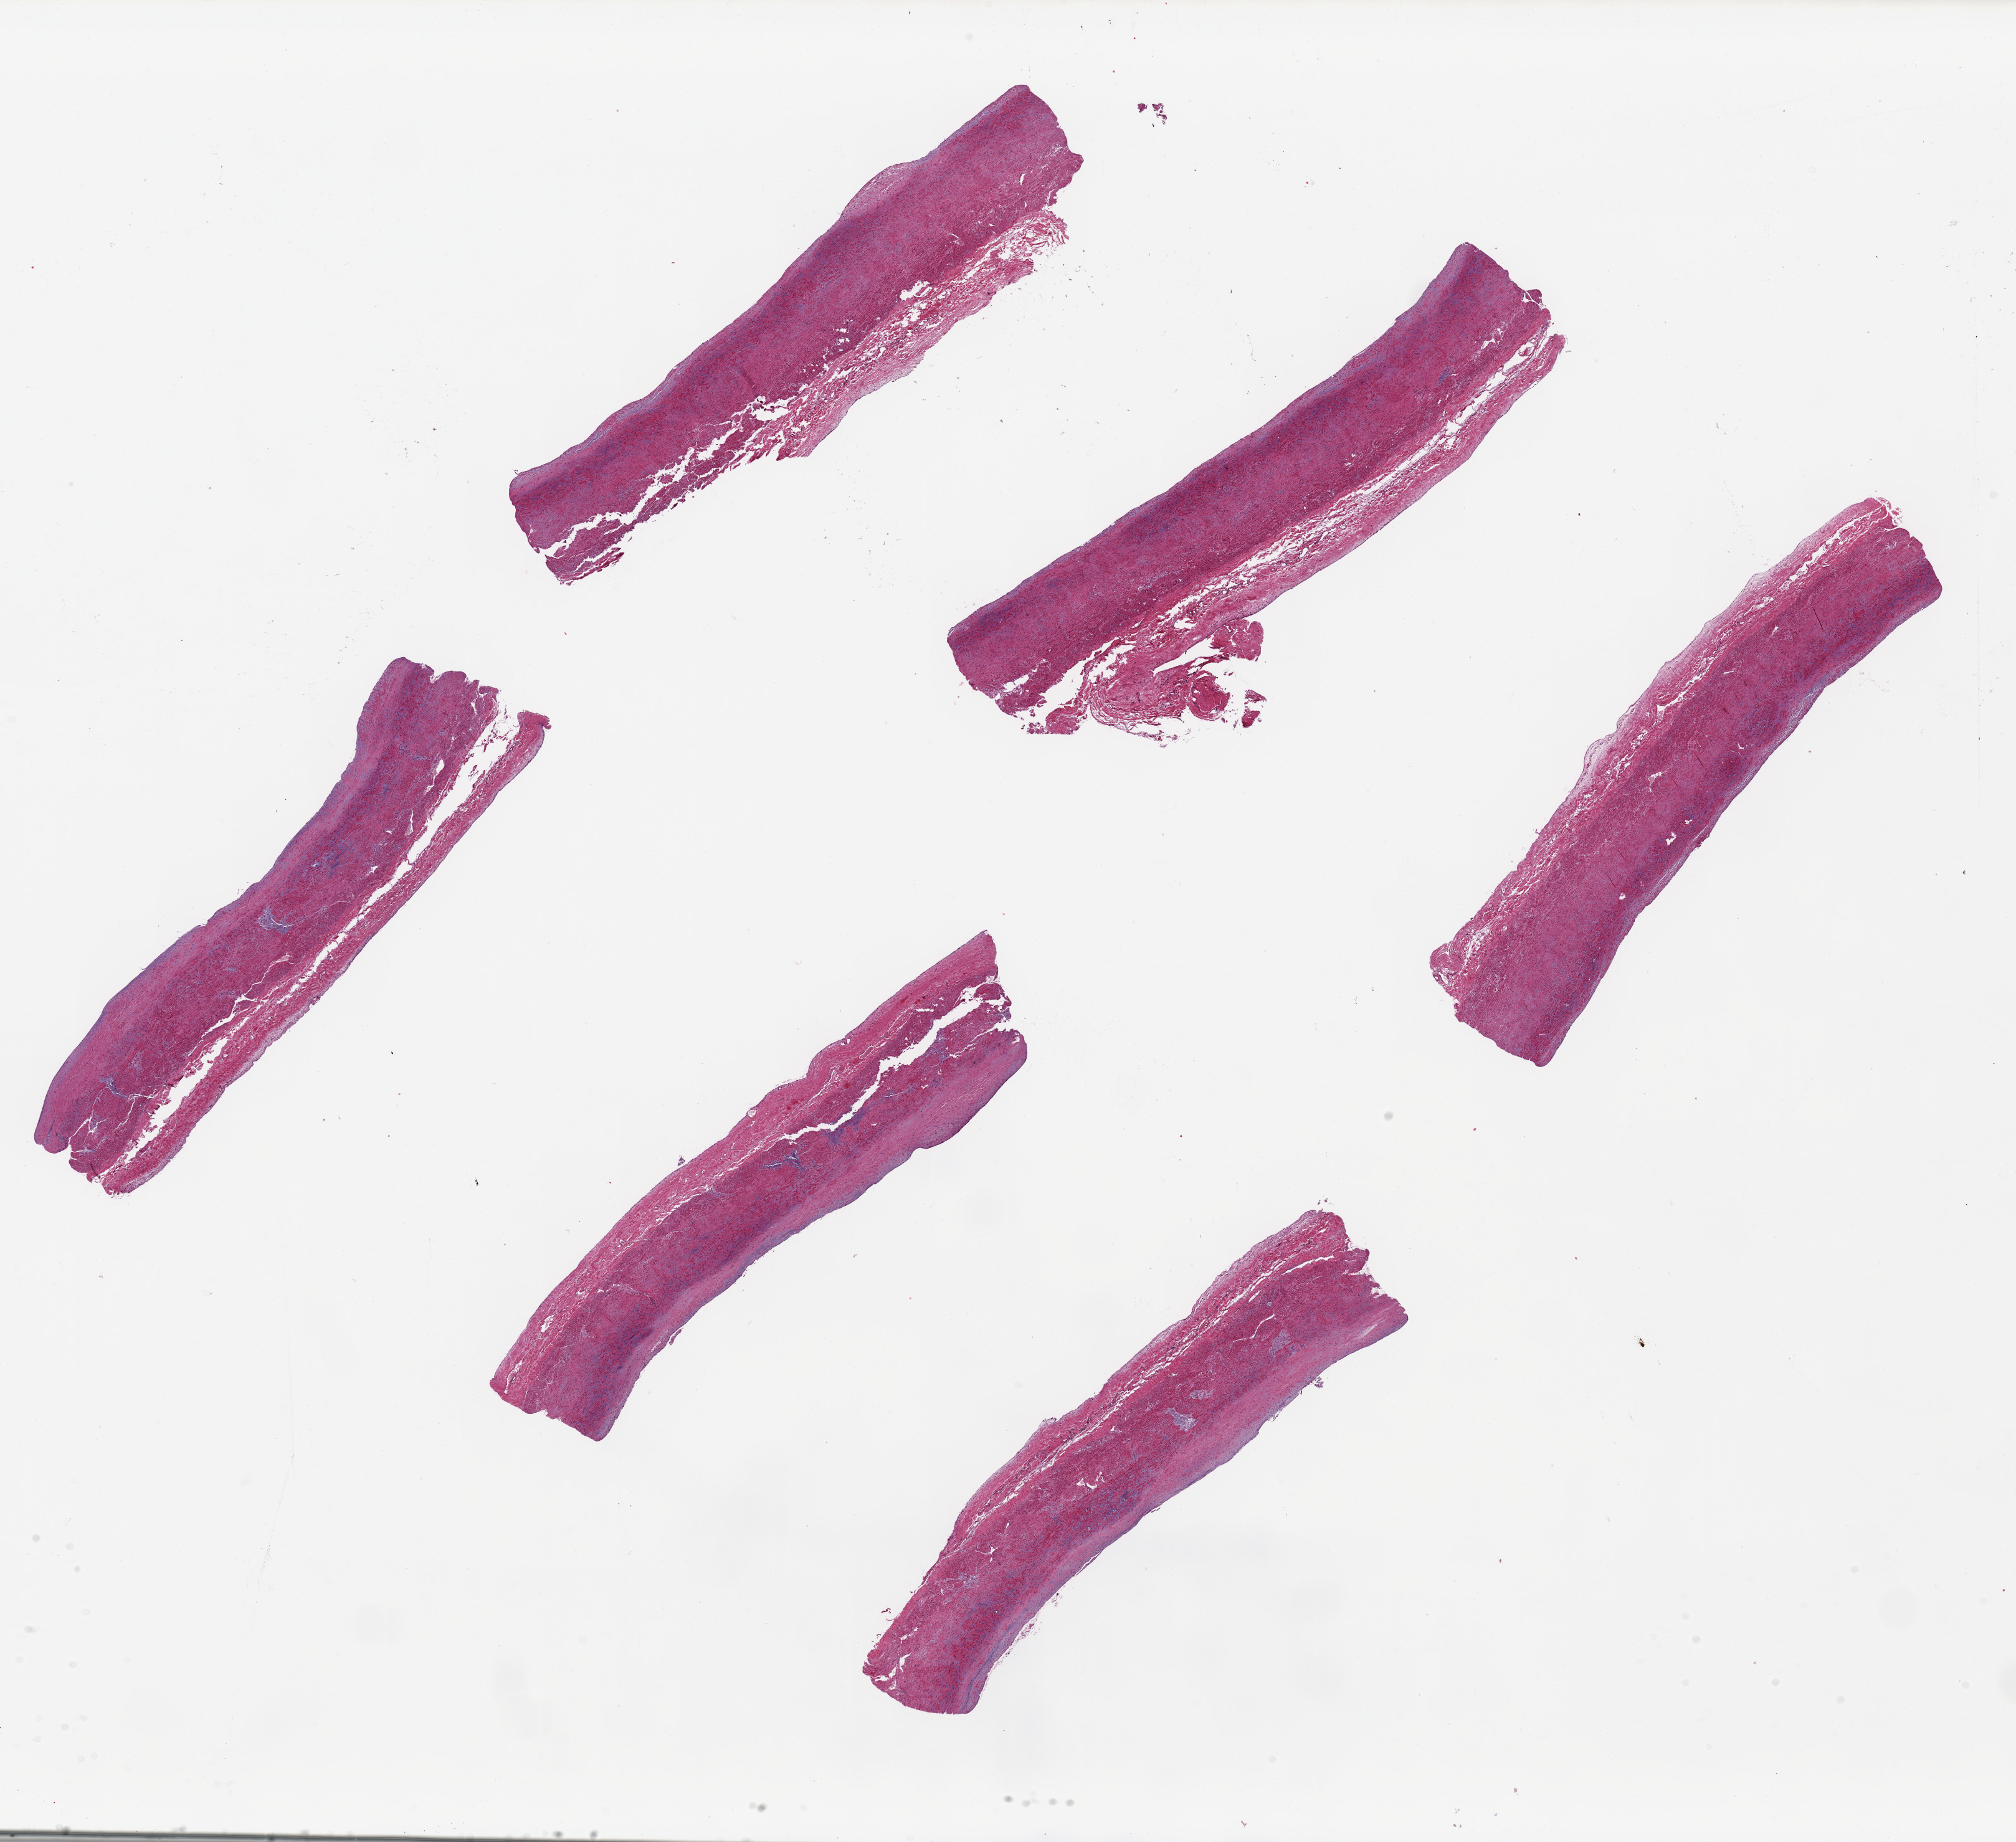
Digitized hematoxylin and eosin (H&E)-stained section — shown as a low-resolution overview of the whole scanned area (about 25.6 x 23.4 mm). PAXgene-fixed, paraffin-embedded tissue. Target tissue: aorta. Donor tissue sample.
* pathologist's review note for this sample: 6 ~8x1.5mm pieces, mild patchy atherosis